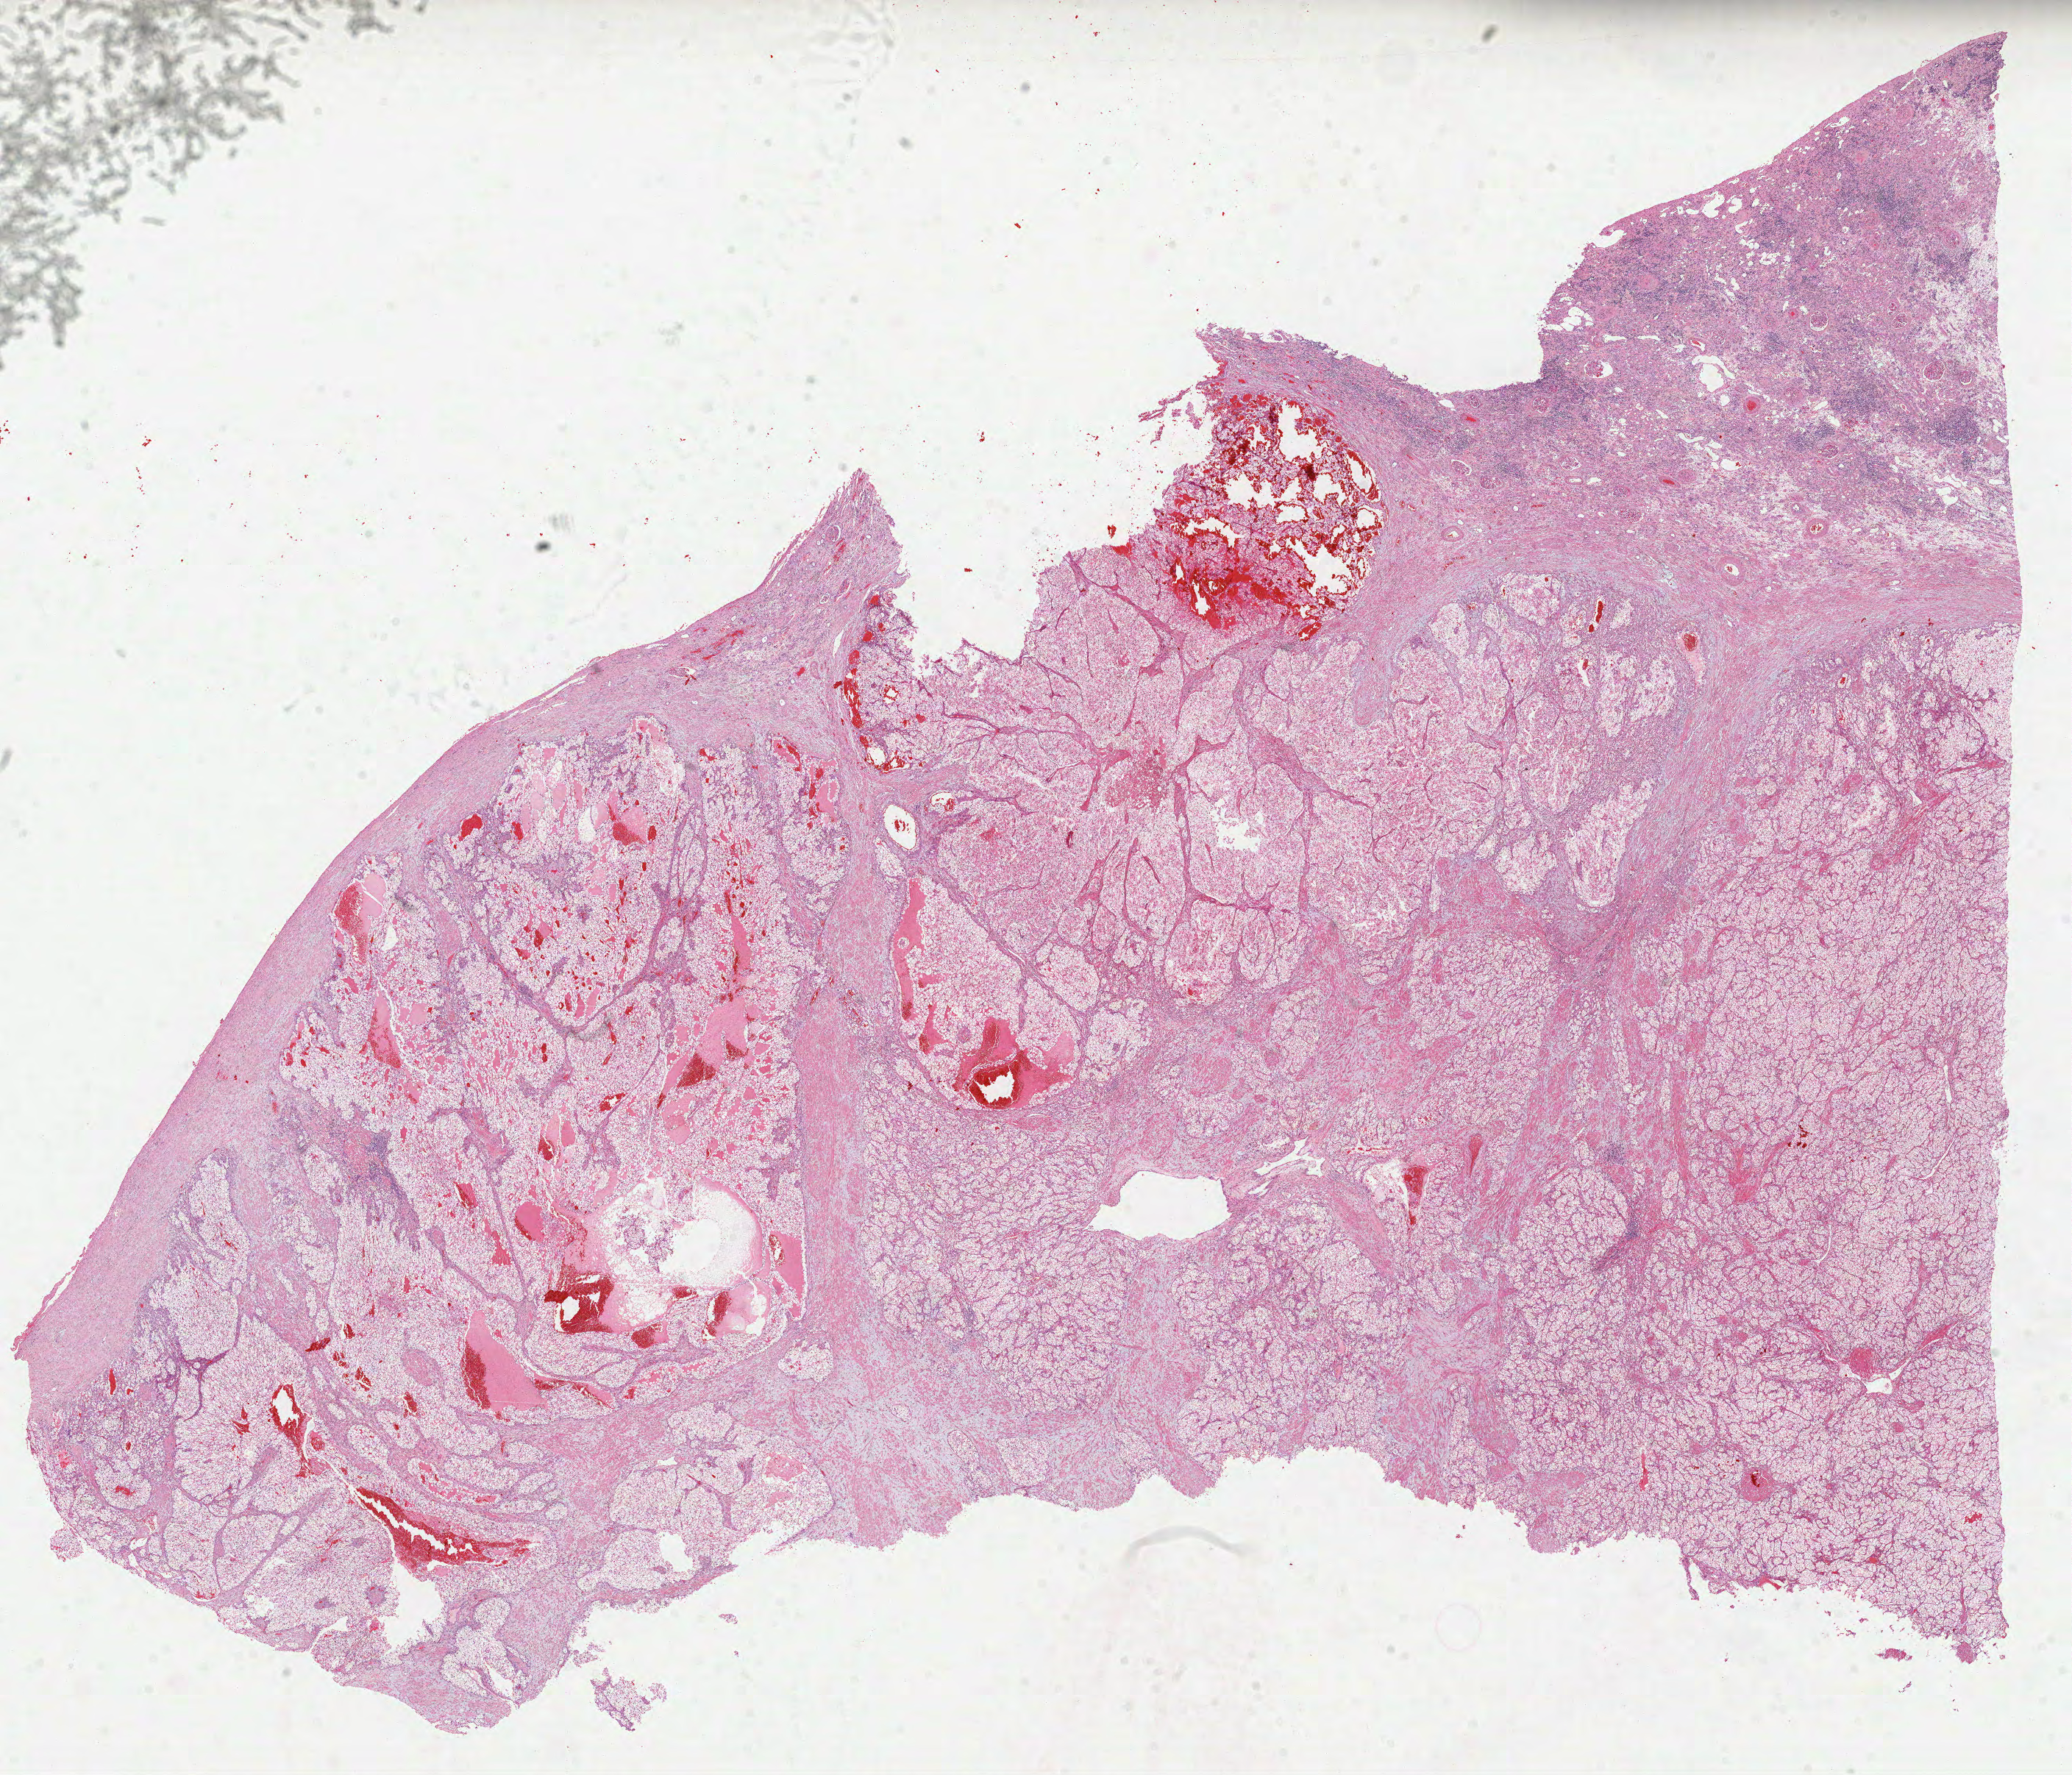
H&E whole-slide image, whole scanned area (about 22.7 x 19.5 mm, from a 40x scan) shown as a low-resolution overview; formalin-fixed paraffin-embedded (FFPE) diagnostic section; primary tumour sample from the kidney. Male patient; age at initial diagnosis 57 years. Histologic grade: G3 (poorly differentiated).
* diagnosis: Clear cell adenocarcinoma, NOS
* AJCC pathologic stage: III (6th edition)